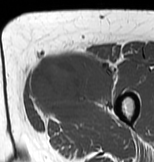
MRI of an extremity soft-tissue mass, one axial slice. Slice 25 of 83 in the series (ordered by position). MR volume resampled by the dataset authors to the PET/CT grid (not the native acquisition matrix). 3.27 mm slice thickness. 154 × 162 image matrix. Female patient. From the clinical record (not read from this slice): histological type: myxofibrosarcoma; grade: intermediate; site of the primary tumour: left thigh.
Structures marked on this image (expert contour drawn on MRI and transferred to this co-registered scan by the dataset authors):
- gross tumour volume including surrounding oedema: bounding box (x1, y1, x2, y2) in pixels: (26, 48, 116, 122)
- gross tumour volume (mass): (30, 54, 114, 120)